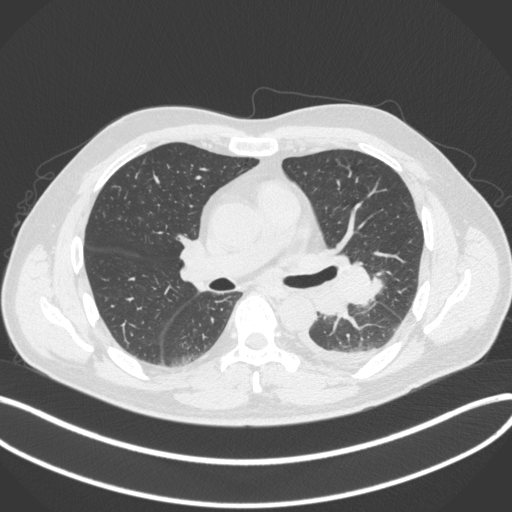
Chest CT, one axial slice. Position 207 of 350 along the scan axis. 120 kVp. Lung window (W 1500 / L -600 HU). 1 mm slice thickness. 512 × 512 image matrix. Male patient, age 58 years. Case-level facts recorded for this patient, not image findings: clinical TNM (as recorded): T3 N1 M1b; histopathological grade: G3.
Annotated regions visible in this slice (bounding box drawn by a radiologist):
- lung tumour (recorded histology: small cell carcinoma): bounding box <304,256,382,314> (left, top, right, bottom; pixels)